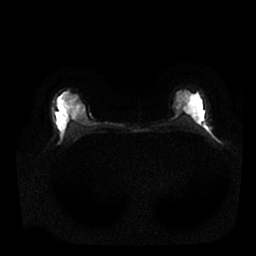
Breast MRI, one axial slice. Position 15 of 25 along the scan axis. Diffusion-weighted series; image 2 of 4 stored at this slice position (different b-values; order by instance number). 1.5 T. 4 mm slice thickness. 256 × 256 image matrix, field of view 320 × 320 mm. Female patient.
Structures marked on this image (outlined manually by an expert reader):
- tumour on diffusion-weighted imaging: bounding box (x1, y1, x2, y2) in pixels: (175, 109, 181, 114)